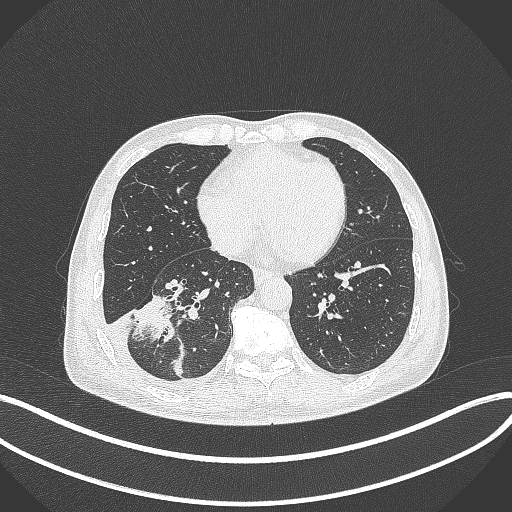
Chest CT, one axial slice. Position 138 of 388 along the scan axis. Reconstruction kernel B70f. 120 kVp. Lung window (W 1500 / L -600 HU). 512 × 512 image matrix. Male patient, age 64 years. From the clinical record (not read from this slice): clinical TNM (as recorded): T3 N0 M0; histopathological grade: G2-3.
Structures marked on this image (rectangle marked by the reading radiologist):
- lung tumour (recorded histology: adenocarcinoma): bounding box [x1, y1, x2, y2] px = [135, 287, 179, 346]